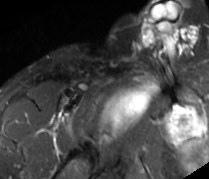
MRI of an extremity soft-tissue mass, one axial slice; position 75 of 89 along the scan axis; STIR; MR volume resampled by the dataset authors to the PET/CT grid (not the native acquisition matrix); 3.27 mm slice thickness; 209 × 179 image matrix. Male patient. Case-level facts recorded for this patient, not image findings: histological type: undifferentiated - pleiomorphic; grade: high; site of the primary tumour: right thigh.
Structures marked on this image (expert contour drawn on MRI and transferred to this co-registered scan by the dataset authors):
- gross tumour volume including surrounding oedema: box from (x=101, y=78) to (x=159, y=138) px
- gross tumour volume (mass): (x=101, y=85)–(x=152, y=133)